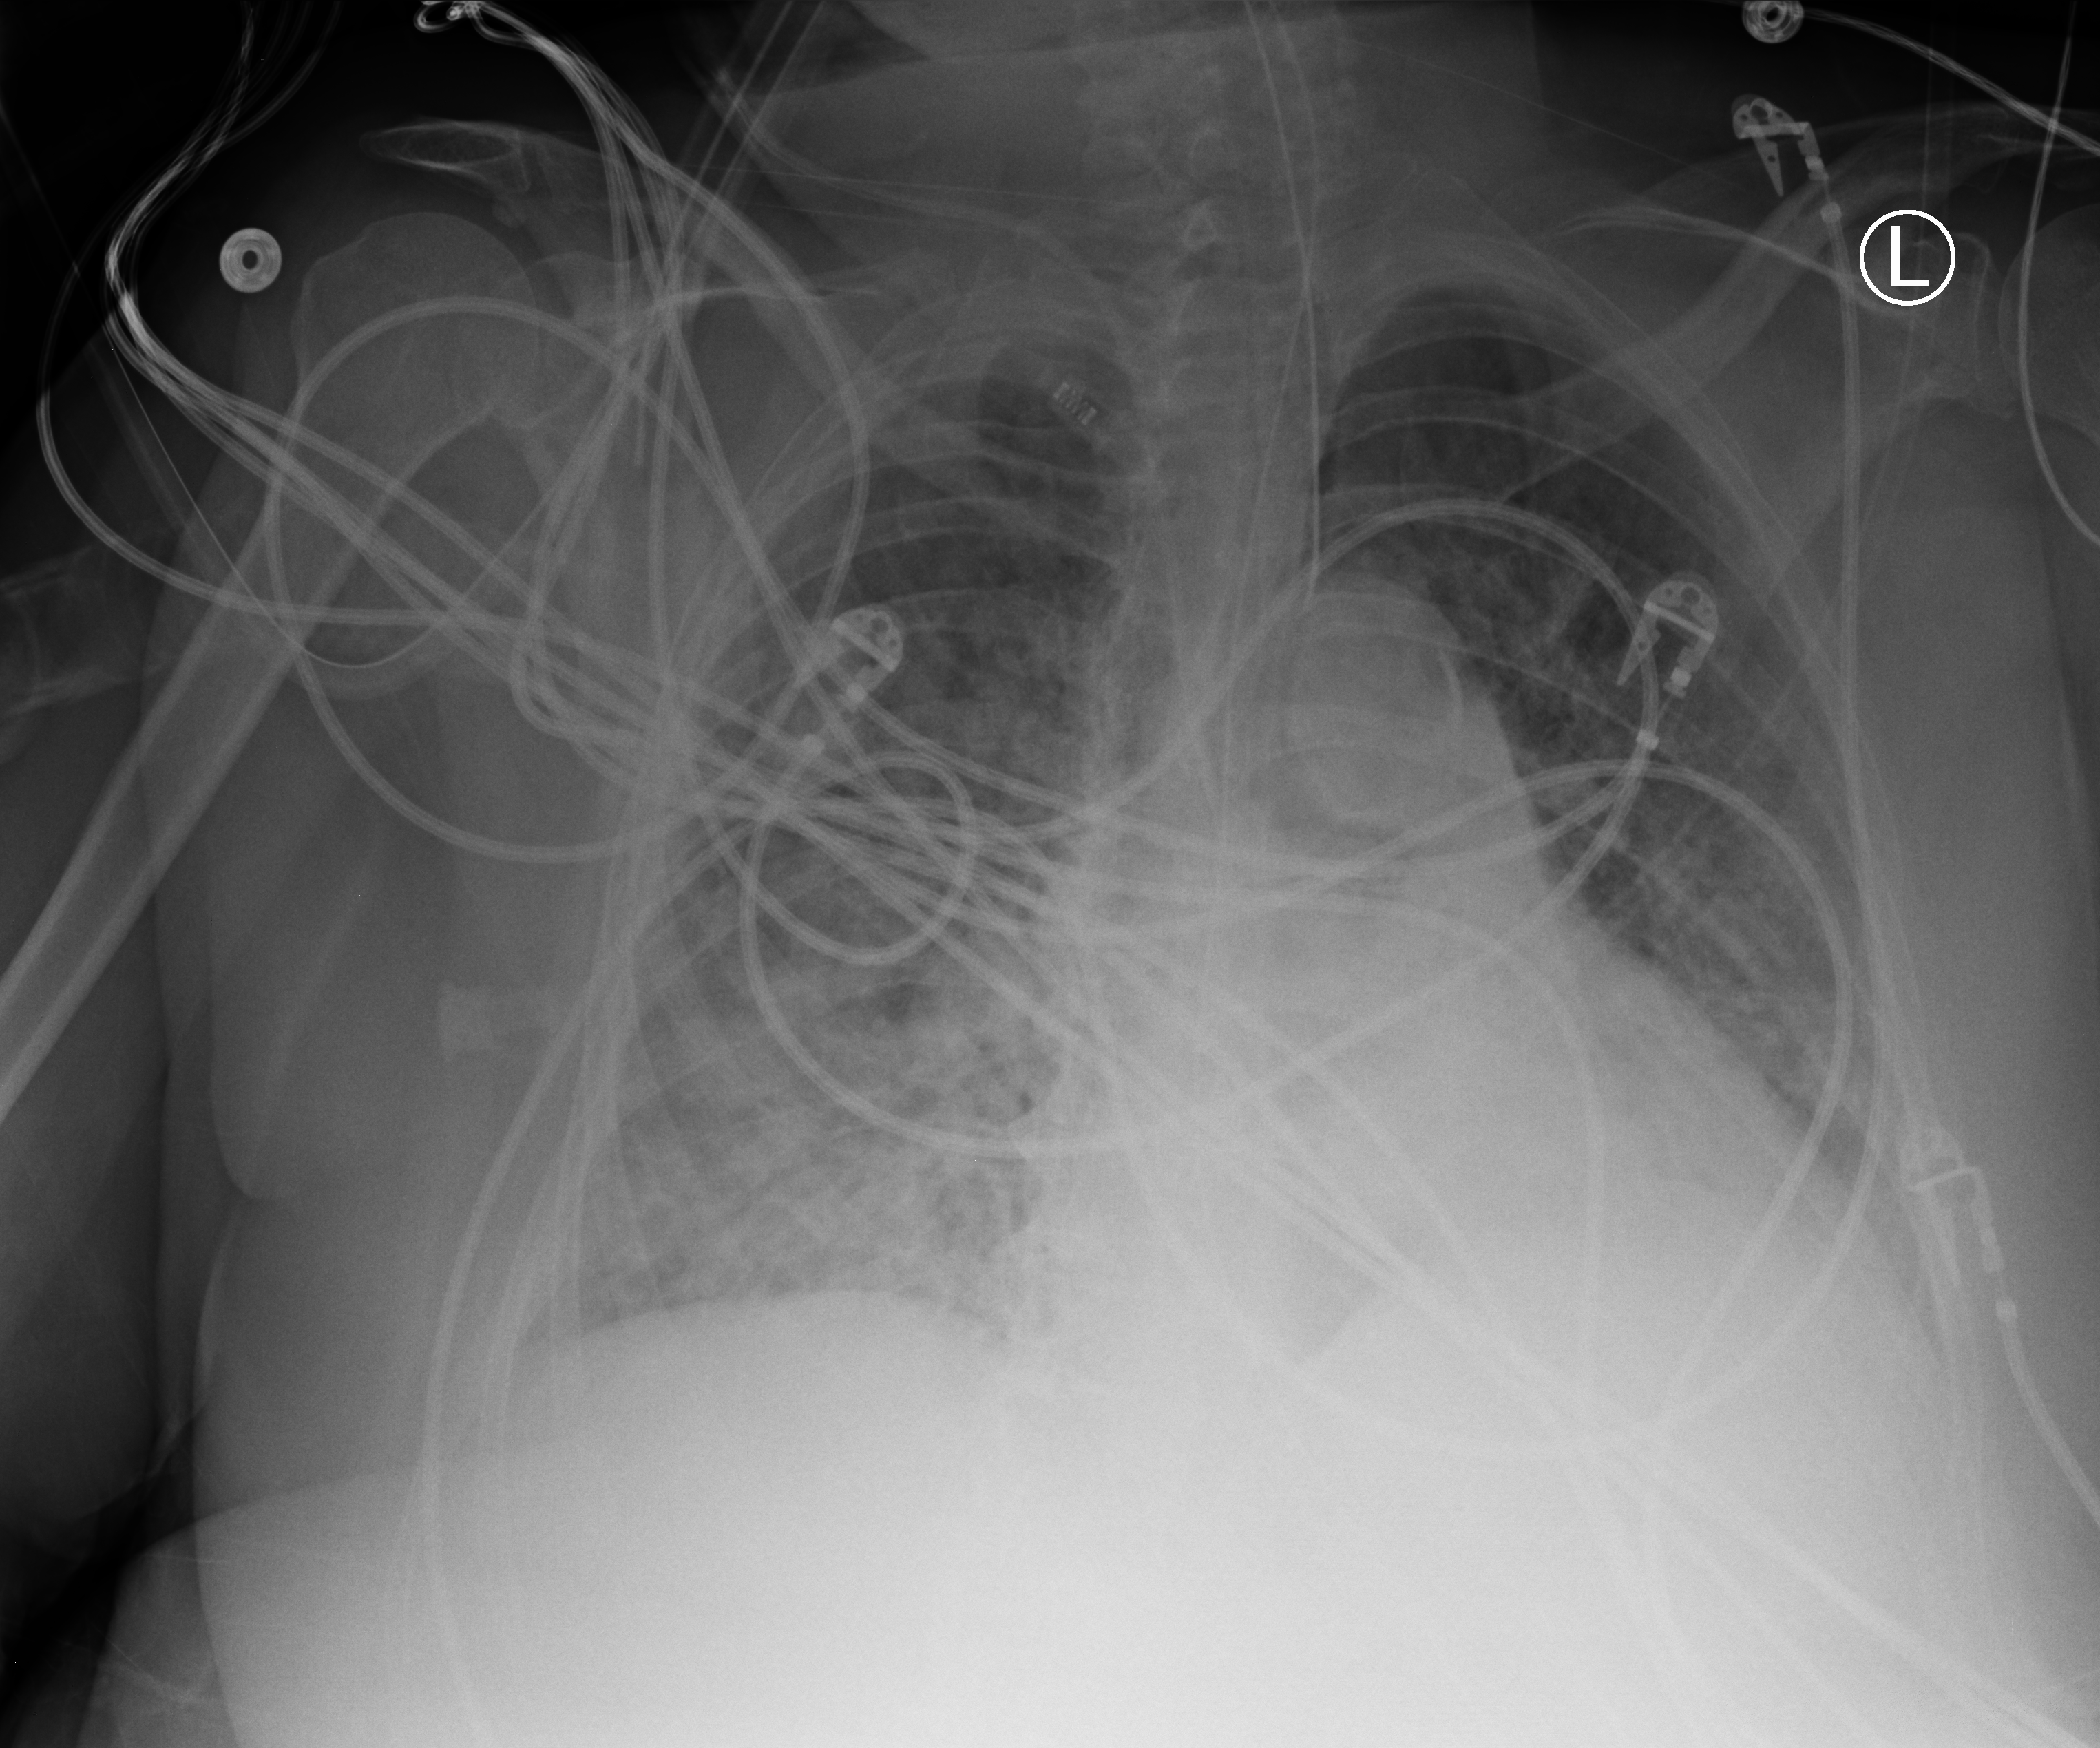
Bedside chest radiograph (computed radiography), anteroposterior (AP) projection. Patient hospitalised with COVID-19; female, aged 75–90 years.
Hospital-stay facts (about this admission, not read from this image; timing relative to this image not recorded): hypertension (admission record): yes; mechanically ventilated during this hospital stay: yes.